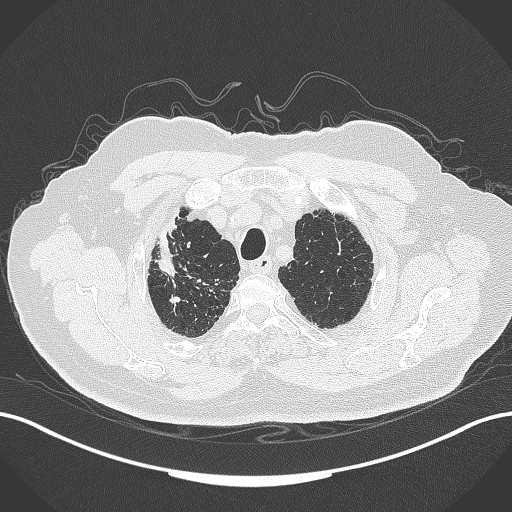
Chest CT, one axial slice; position 306 of 389 along the scan axis; reconstruction kernel B70f; 120 kVp; lung window (W 1500 / L -600 HU); 512 × 512 image matrix, field of view 400 × 400 mm. Patient: male, 72 years. Case-level facts recorded for this patient, not image findings: clinical TNM (as recorded): T1a N0 M0.
Structures marked on this image (rectangle marked by the reading radiologist):
- lung tumour (recorded histology: squamous cell carcinoma): bounding box (x1, y1, x2, y2) in pixels: (156, 204, 183, 280)